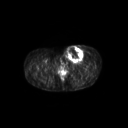
FDG PET of an extremity soft-tissue mass (from a PET/CT study), one axial slice. Slice 55 of 267 in the series (ordered by position). 3.27 mm slice thickness. 128 × 128 image matrix. Patient: female, 24 years. Case-level facts recorded for this patient, not image findings: histological type: leiomyosarcoma; grade: high; site of the primary tumour: groin.
Structures marked on this image (expert contour drawn on MRI and transferred to this co-registered scan by the dataset authors):
- gross tumour volume including surrounding oedema: bounding box <63,44,87,63> (left, top, right, bottom; pixels)
- gross tumour volume (mass): <66,45,84,62>